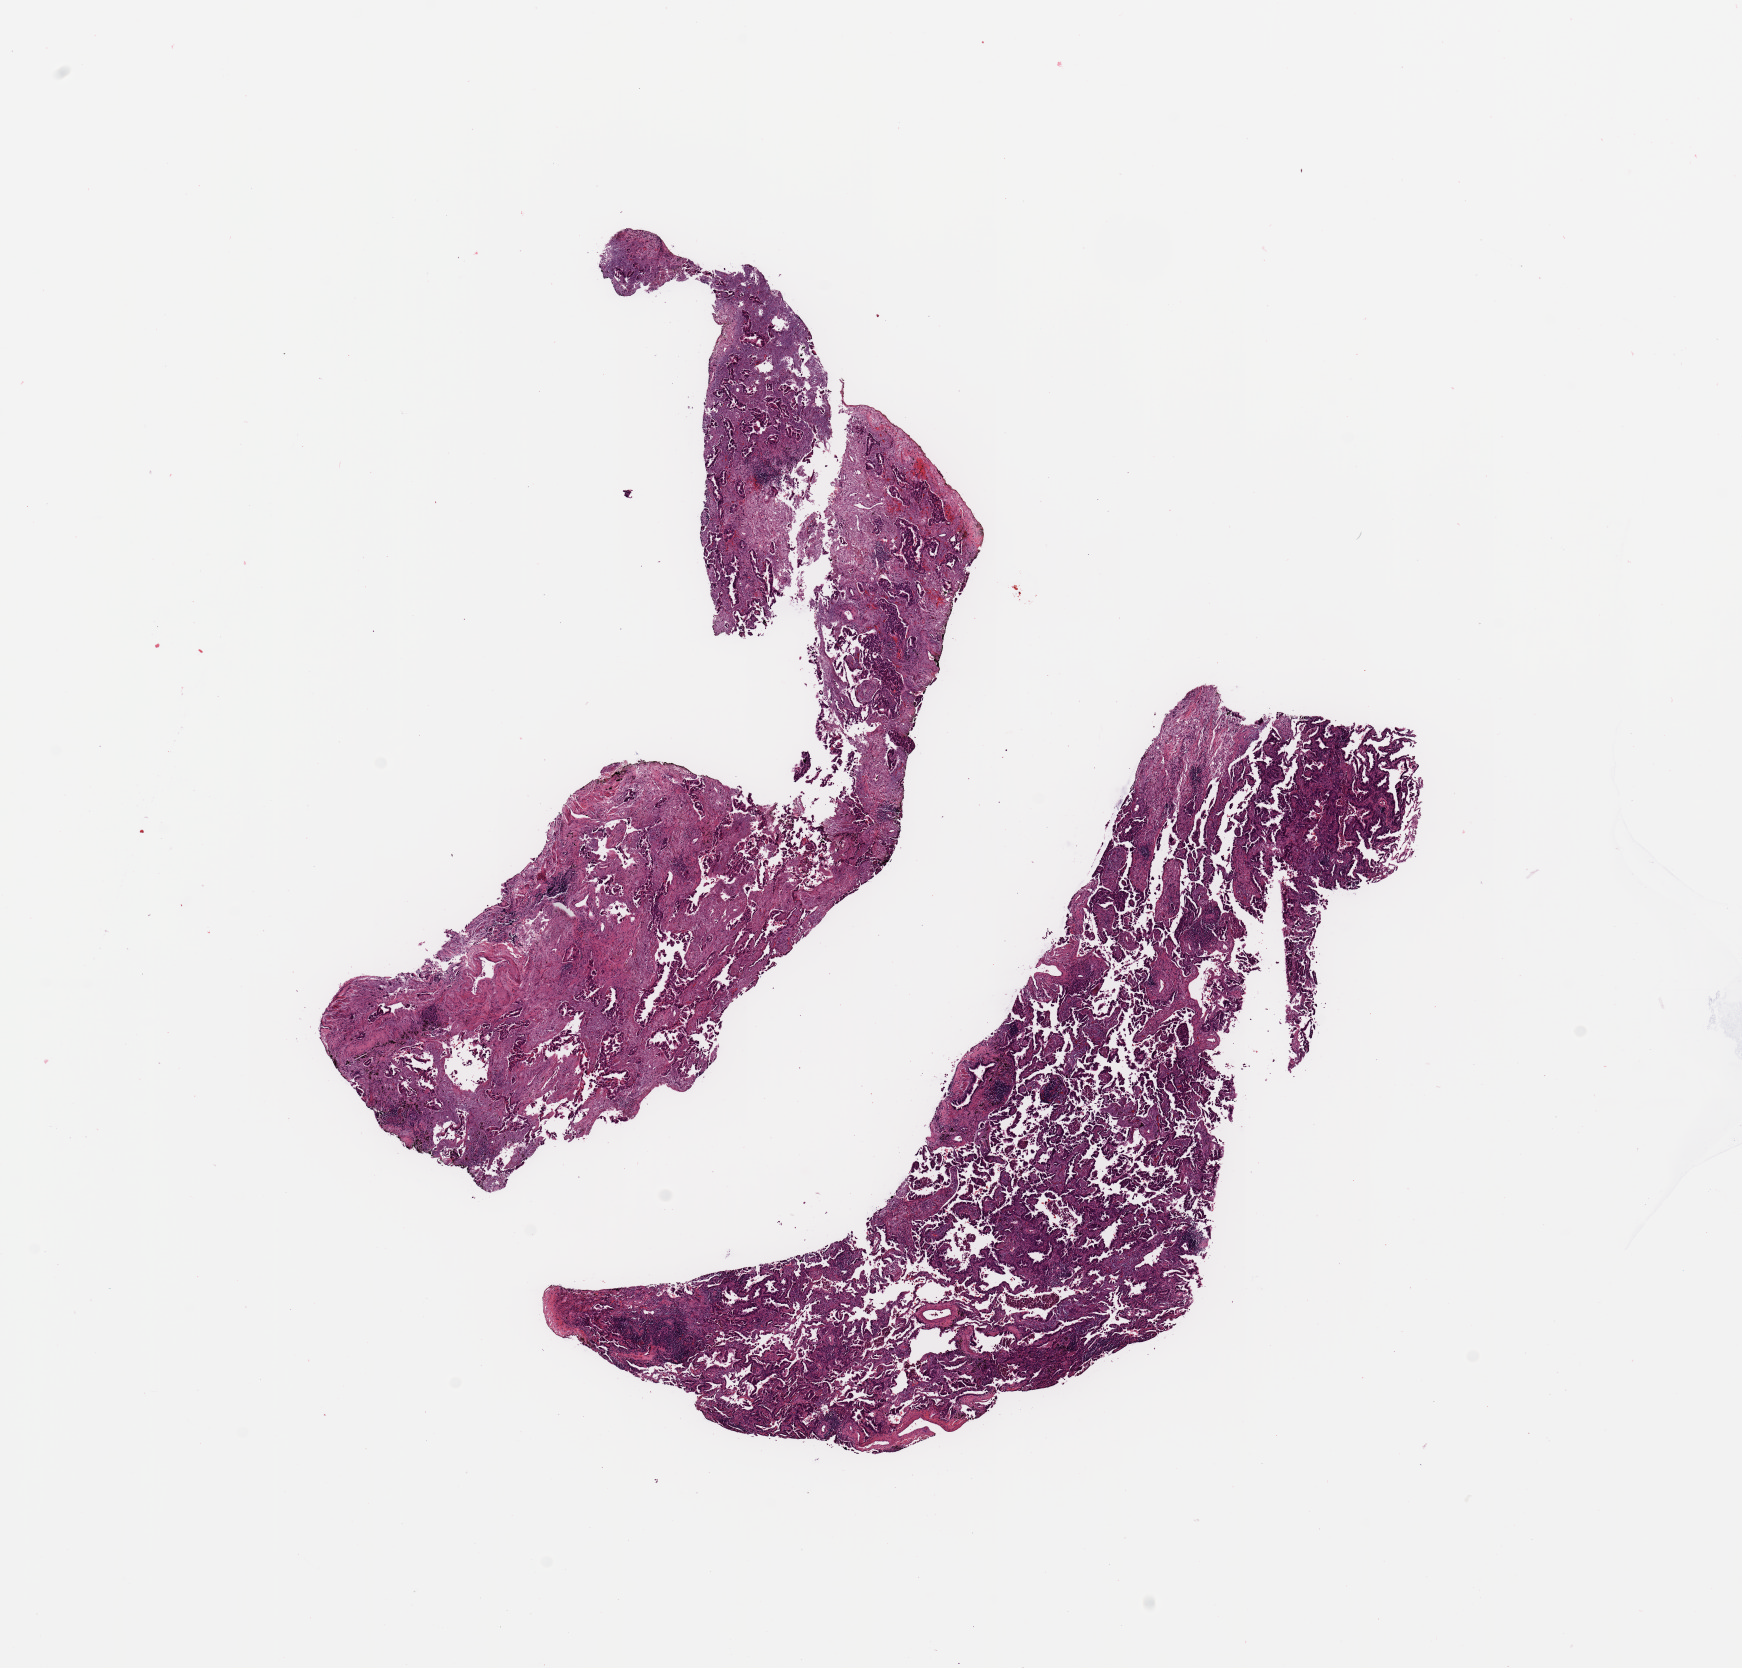
Whole-slide histology image, H&E-stained, shown as a low-resolution overview of the whole scanned area (about 13.8 x 13.2 mm, from a 20x scan); lung, tumour tissue. Patient: female, age 67 years. Histologic grade: G2 (moderately differentiated).
Primary tumour site (as recorded): left upper lobe. AJCC pathologic stage: IB. Diagnosis: Adenocarcinoma, NOS.